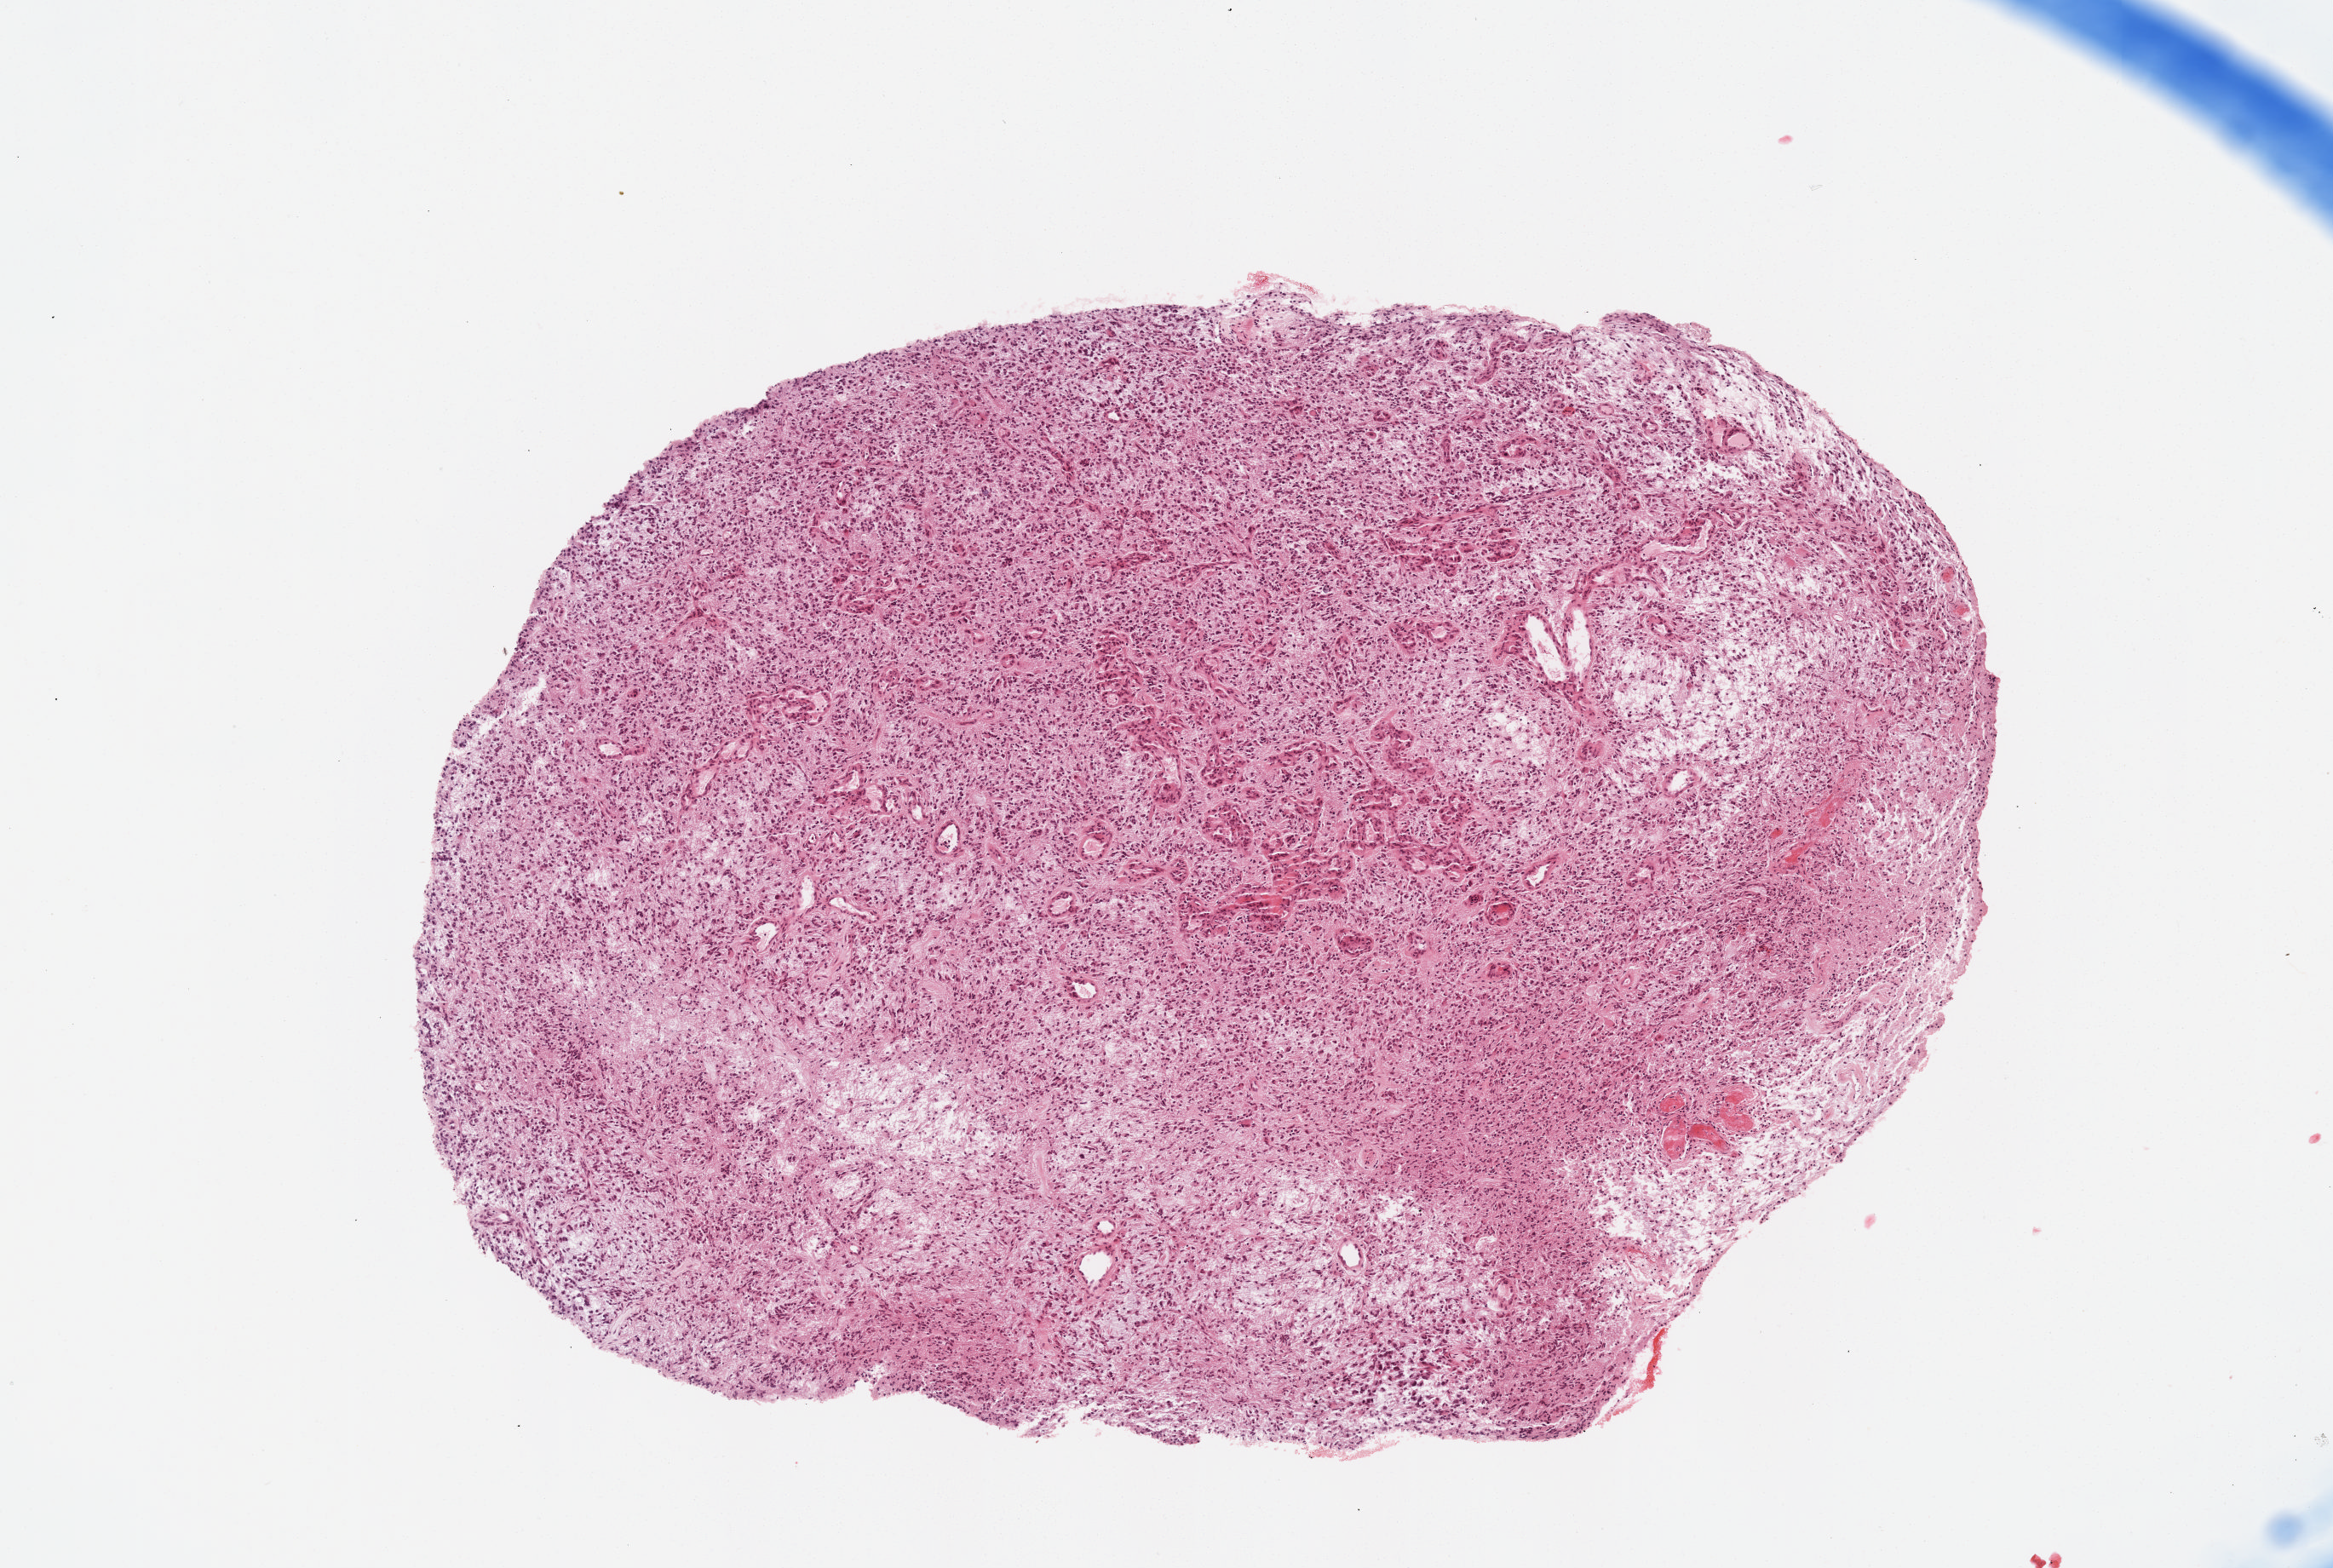
Whole-slide histology image, H&E — shown as a low-resolution overview of the whole scanned area (about 5.5 x 3.7 mm); formalin-fixed paraffin-embedded (FFPE) diagnostic section; brain, primary tumour sample. Male patient; age at initial diagnosis 63 years.
Pathologic diagnosis: Glioblastoma.